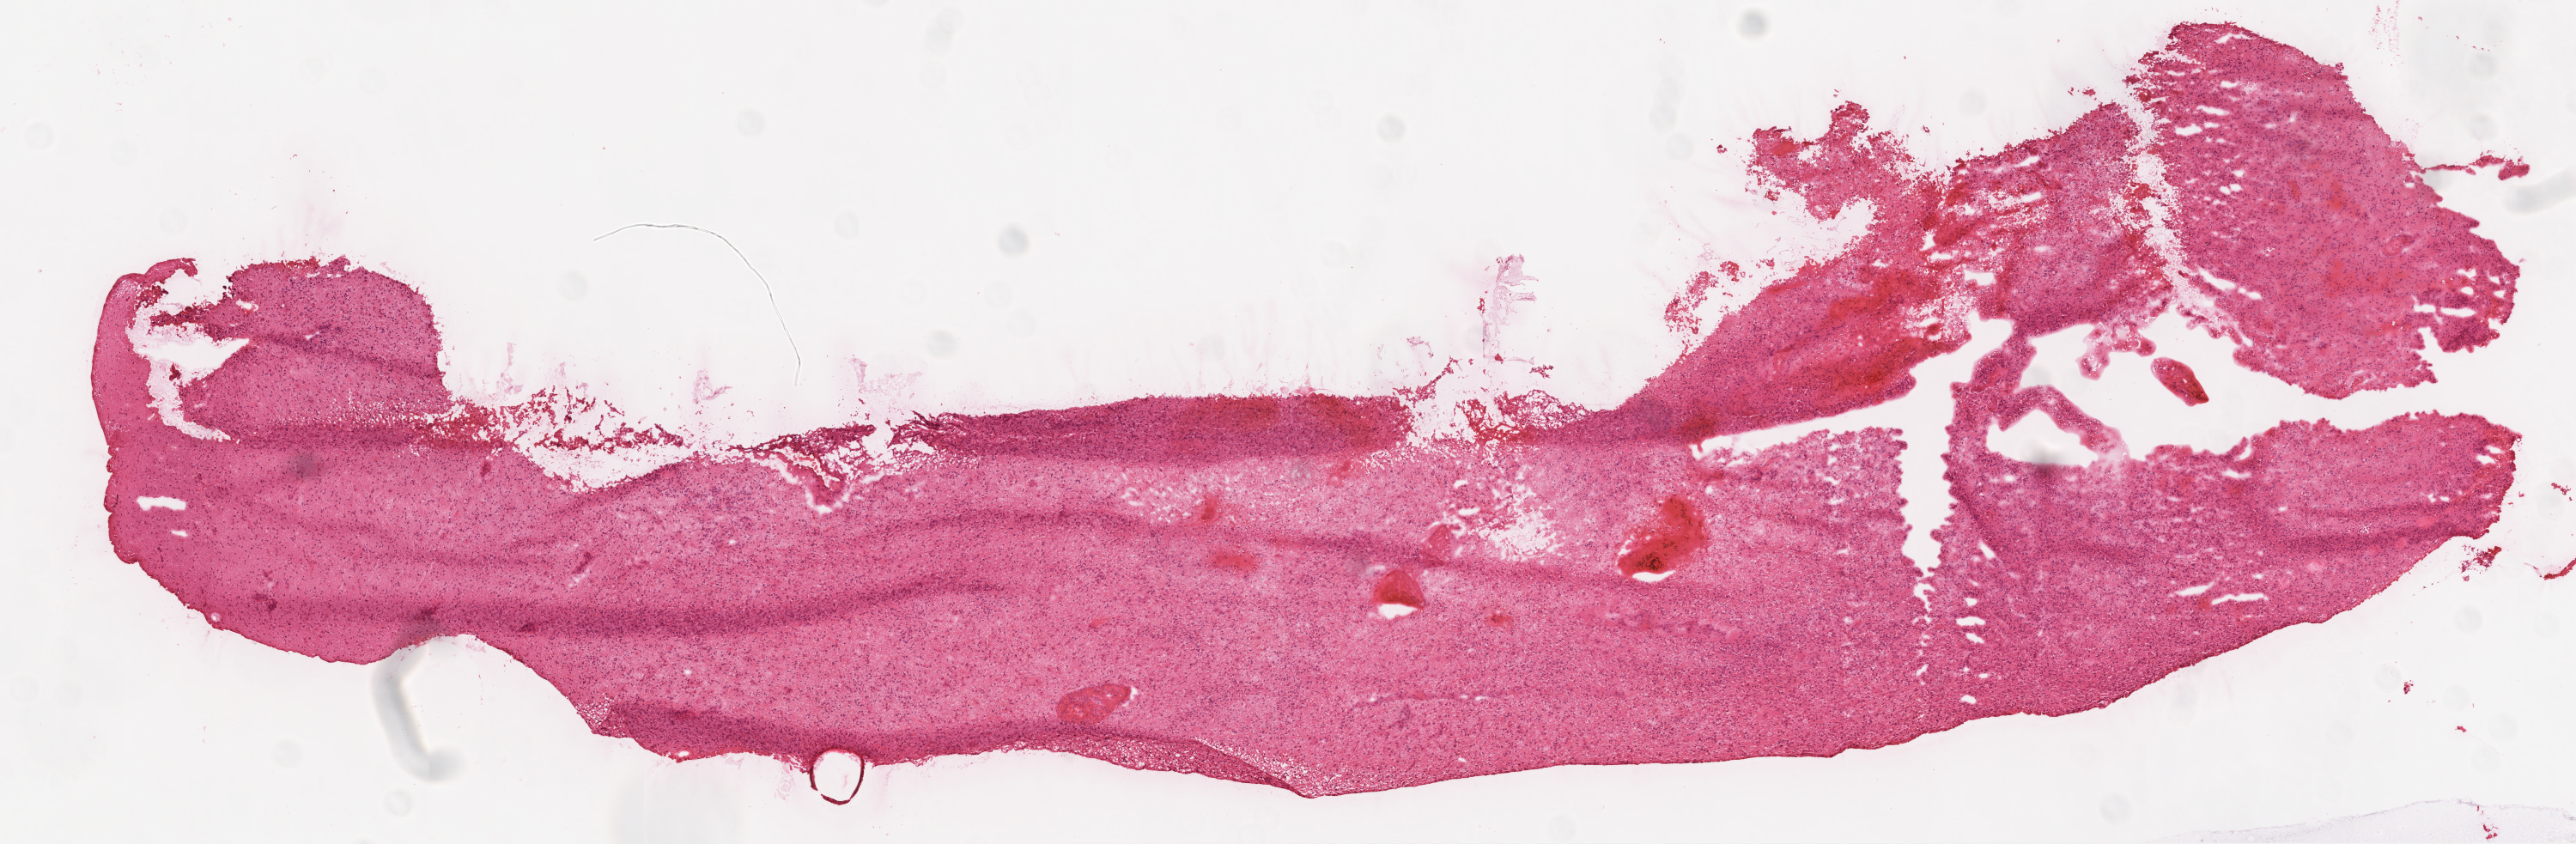
Hematoxylin and eosin (H&E) stained whole-slide image, shown as a low-resolution overview of the whole scanned area (about 12.0 x 3.9 mm, acquisition: 20x scan); frozen section from the top of the tissue portion; primary tumour sample from the brain. Male, age 61 years at initial diagnosis. Composition of this section per pathologist review: tumour cells 80%, tumour nuclei 80%, normal cells 10%, stromal cells 10%, necrosis 0%.
* histologic diagnosis: Glioblastoma